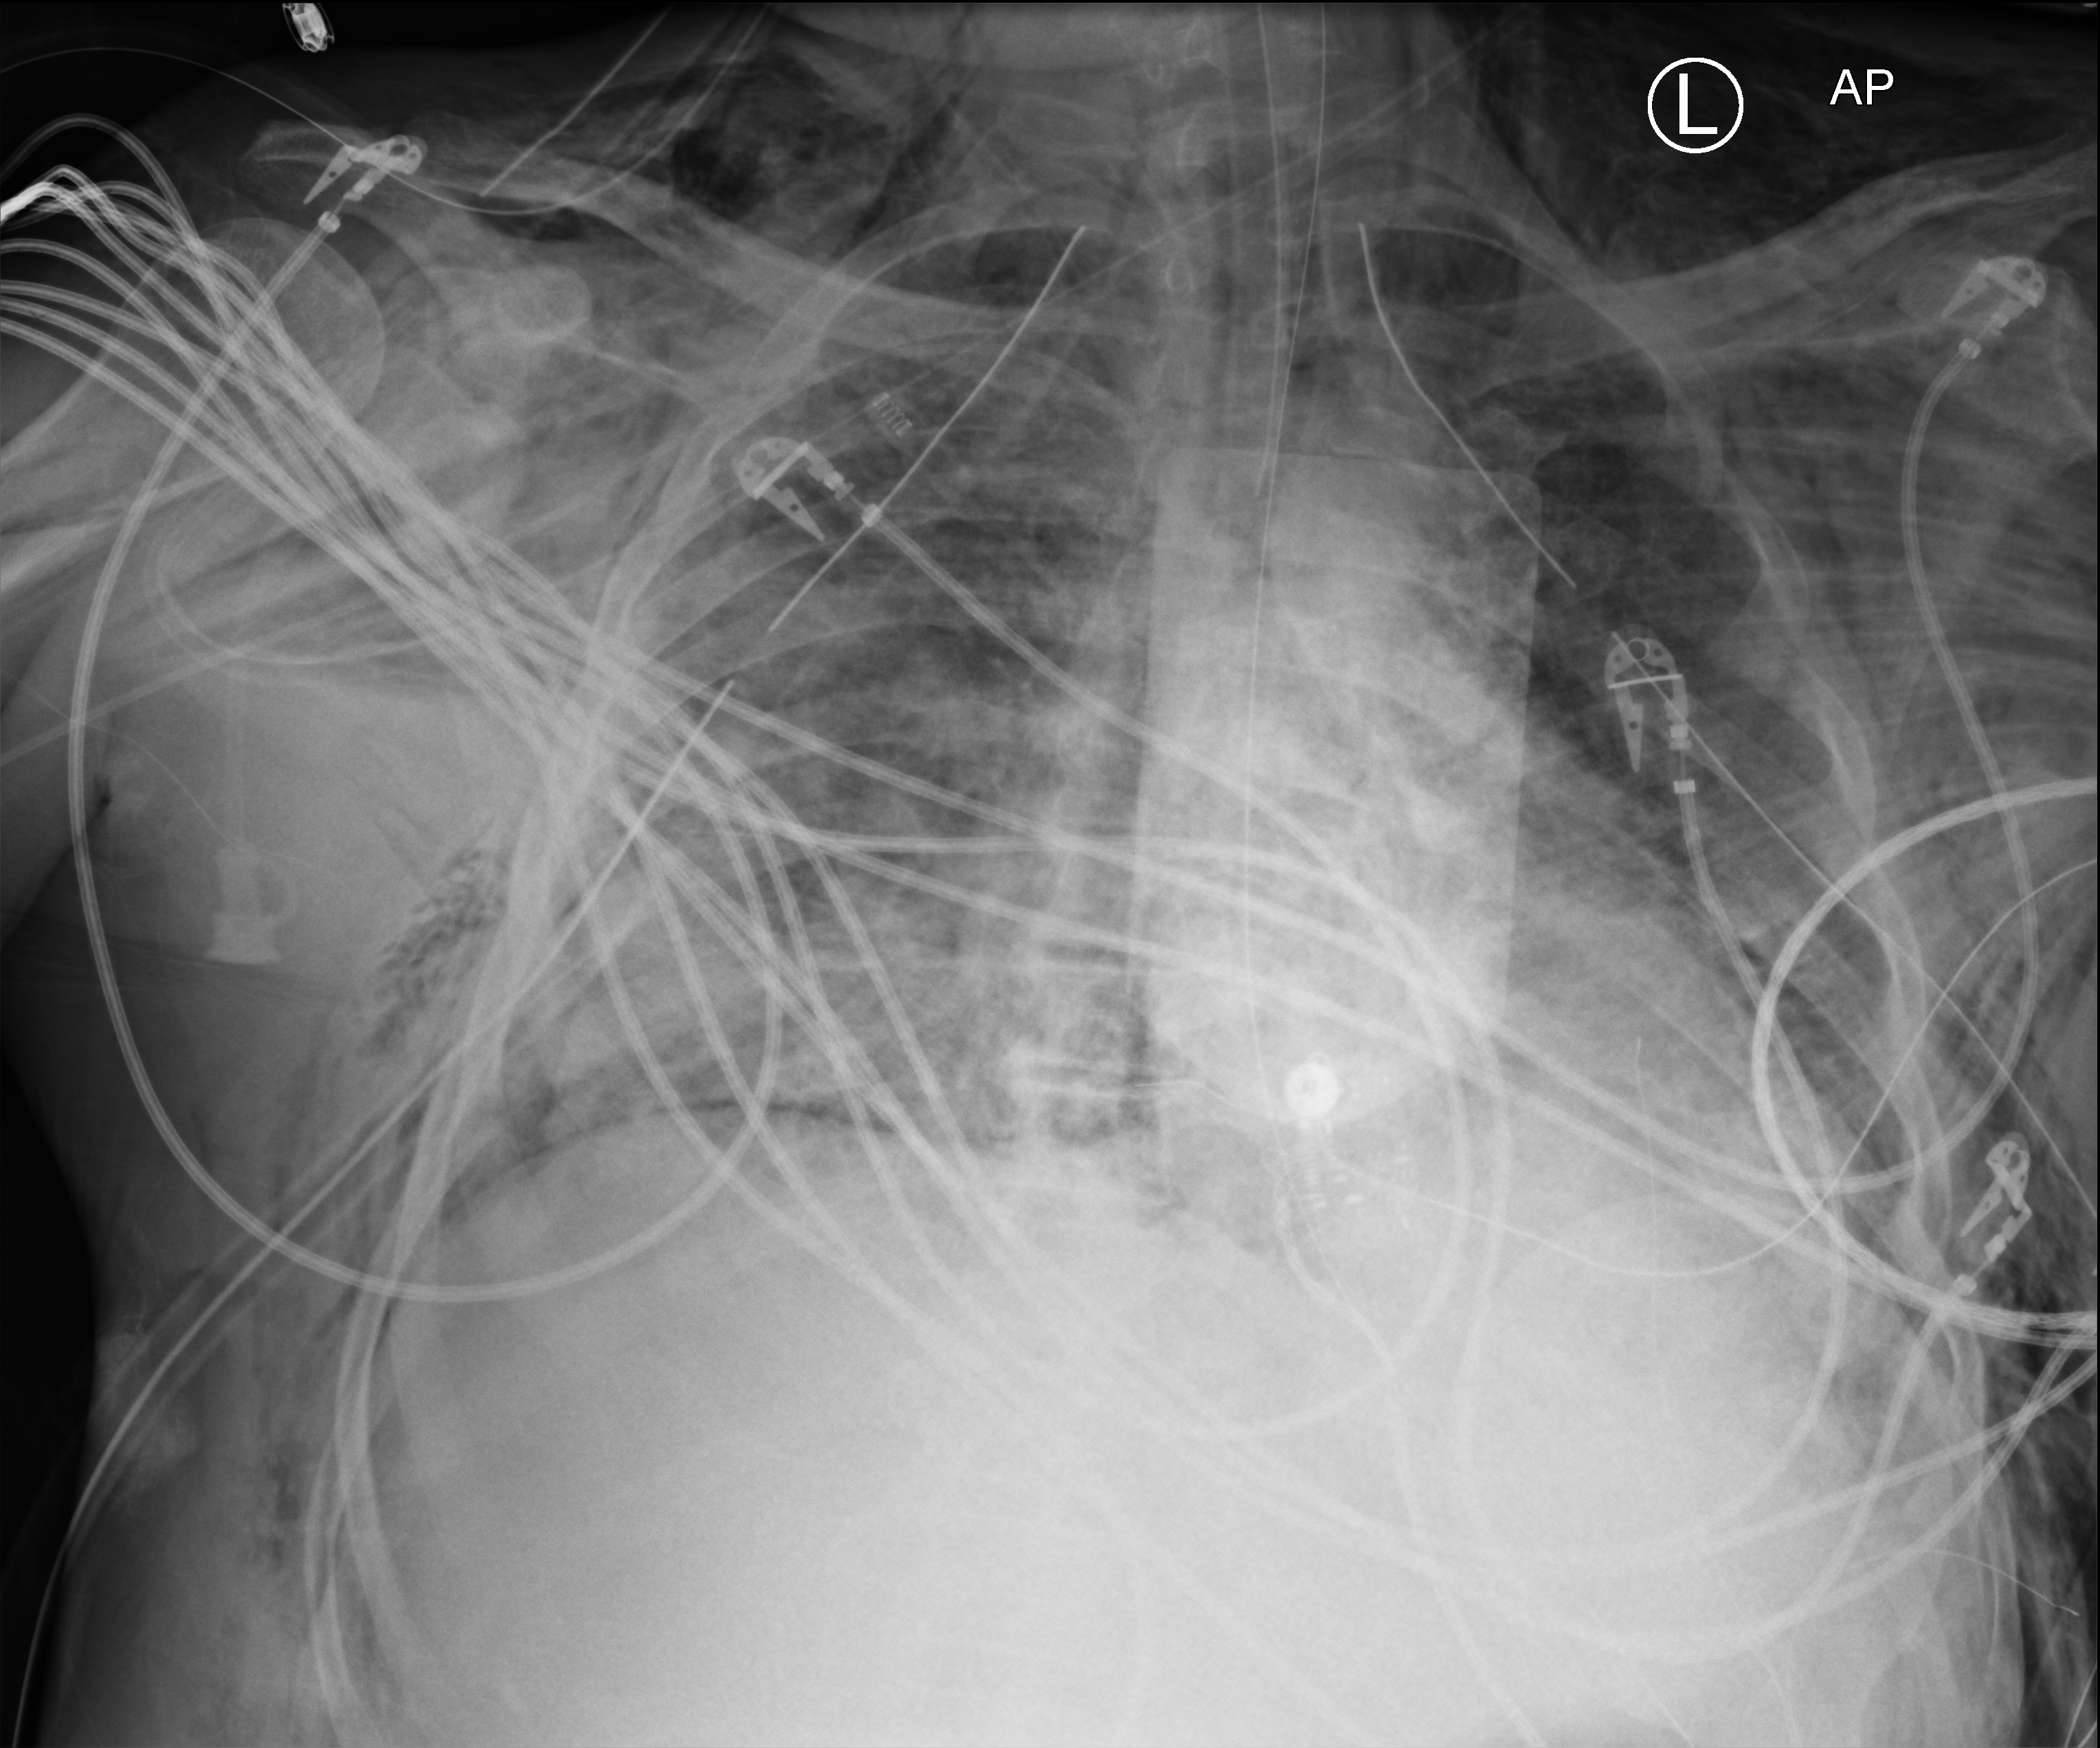
Bedside chest radiograph (computed radiography), anteroposterior (AP) projection. Male patient hospitalised with COVID-19, age 18–59 years.
Hospital-stay facts (about this admission, not read from this image; timing relative to this image not recorded): hypertension (admission record): yes; admitted to intensive care during this hospital stay: yes; COPD (admission record): no.